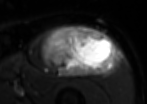
MRI of an extremity soft-tissue mass, one axial slice; slice 54 of 85 in the series (ordered by position); T2-weighted fat-saturated; MR volume resampled by the dataset authors to the PET/CT grid (not the native acquisition matrix); 147 × 104 image matrix, field of view 144 × 102 mm. Male patient. From the clinical record (not read from this slice): histological type: extraskeletal osteosarcoma; grade: high; site of the primary tumour: thigh.
Outlined on this slice (expert contour drawn on MRI and transferred to this co-registered scan by the dataset authors):
- gross tumour volume (mass): bounding box [x1, y1, x2, y2] px = [40, 24, 118, 77]